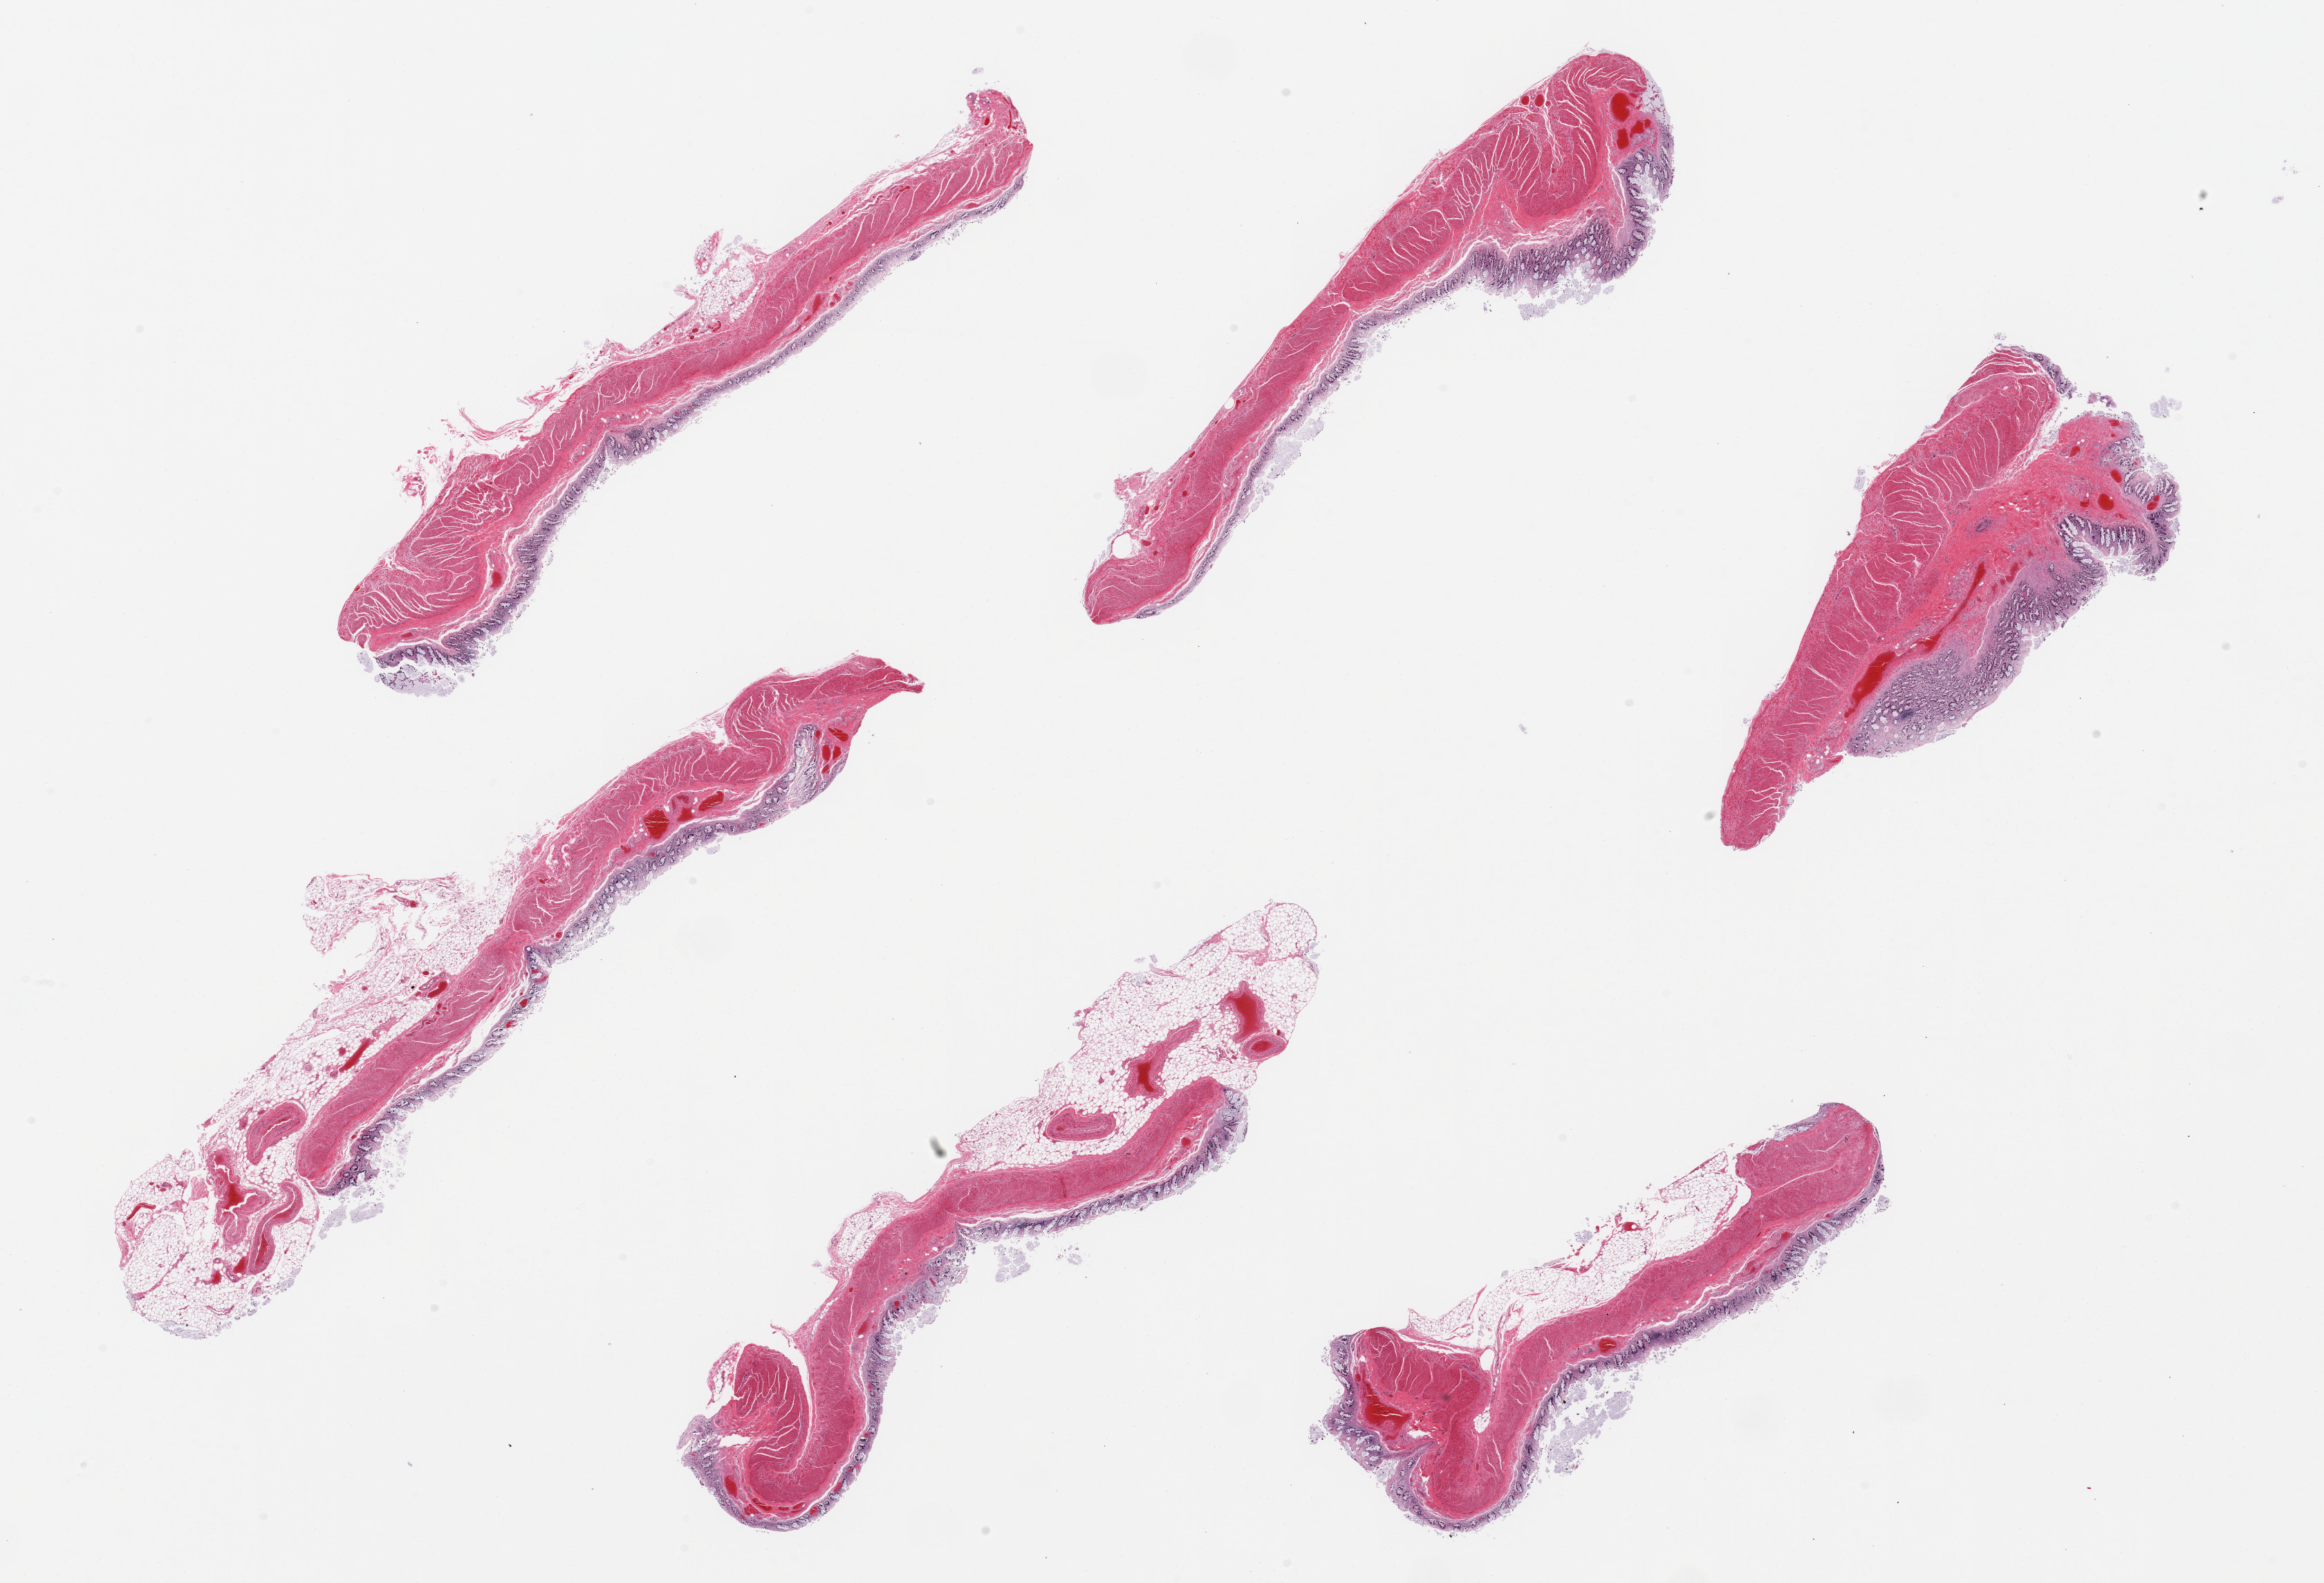
Digitized hematoxylin and eosin (H&E)-stained section, brightfield — a low-resolution overview of the entire scanned area, about 26.6 x 18.1 mm (acquisition: 20x scan), PAXgene-fixed, paraffin-embedded tissue, sampled site (target tissue): transverse colon, donor tissue sample. Donor sex: male.
- pathologist's review note for this sample: 6 pieces; markedly autolyzed mucosa (3) and muscularis (2) with attached fat up to 40% in 3 pieces